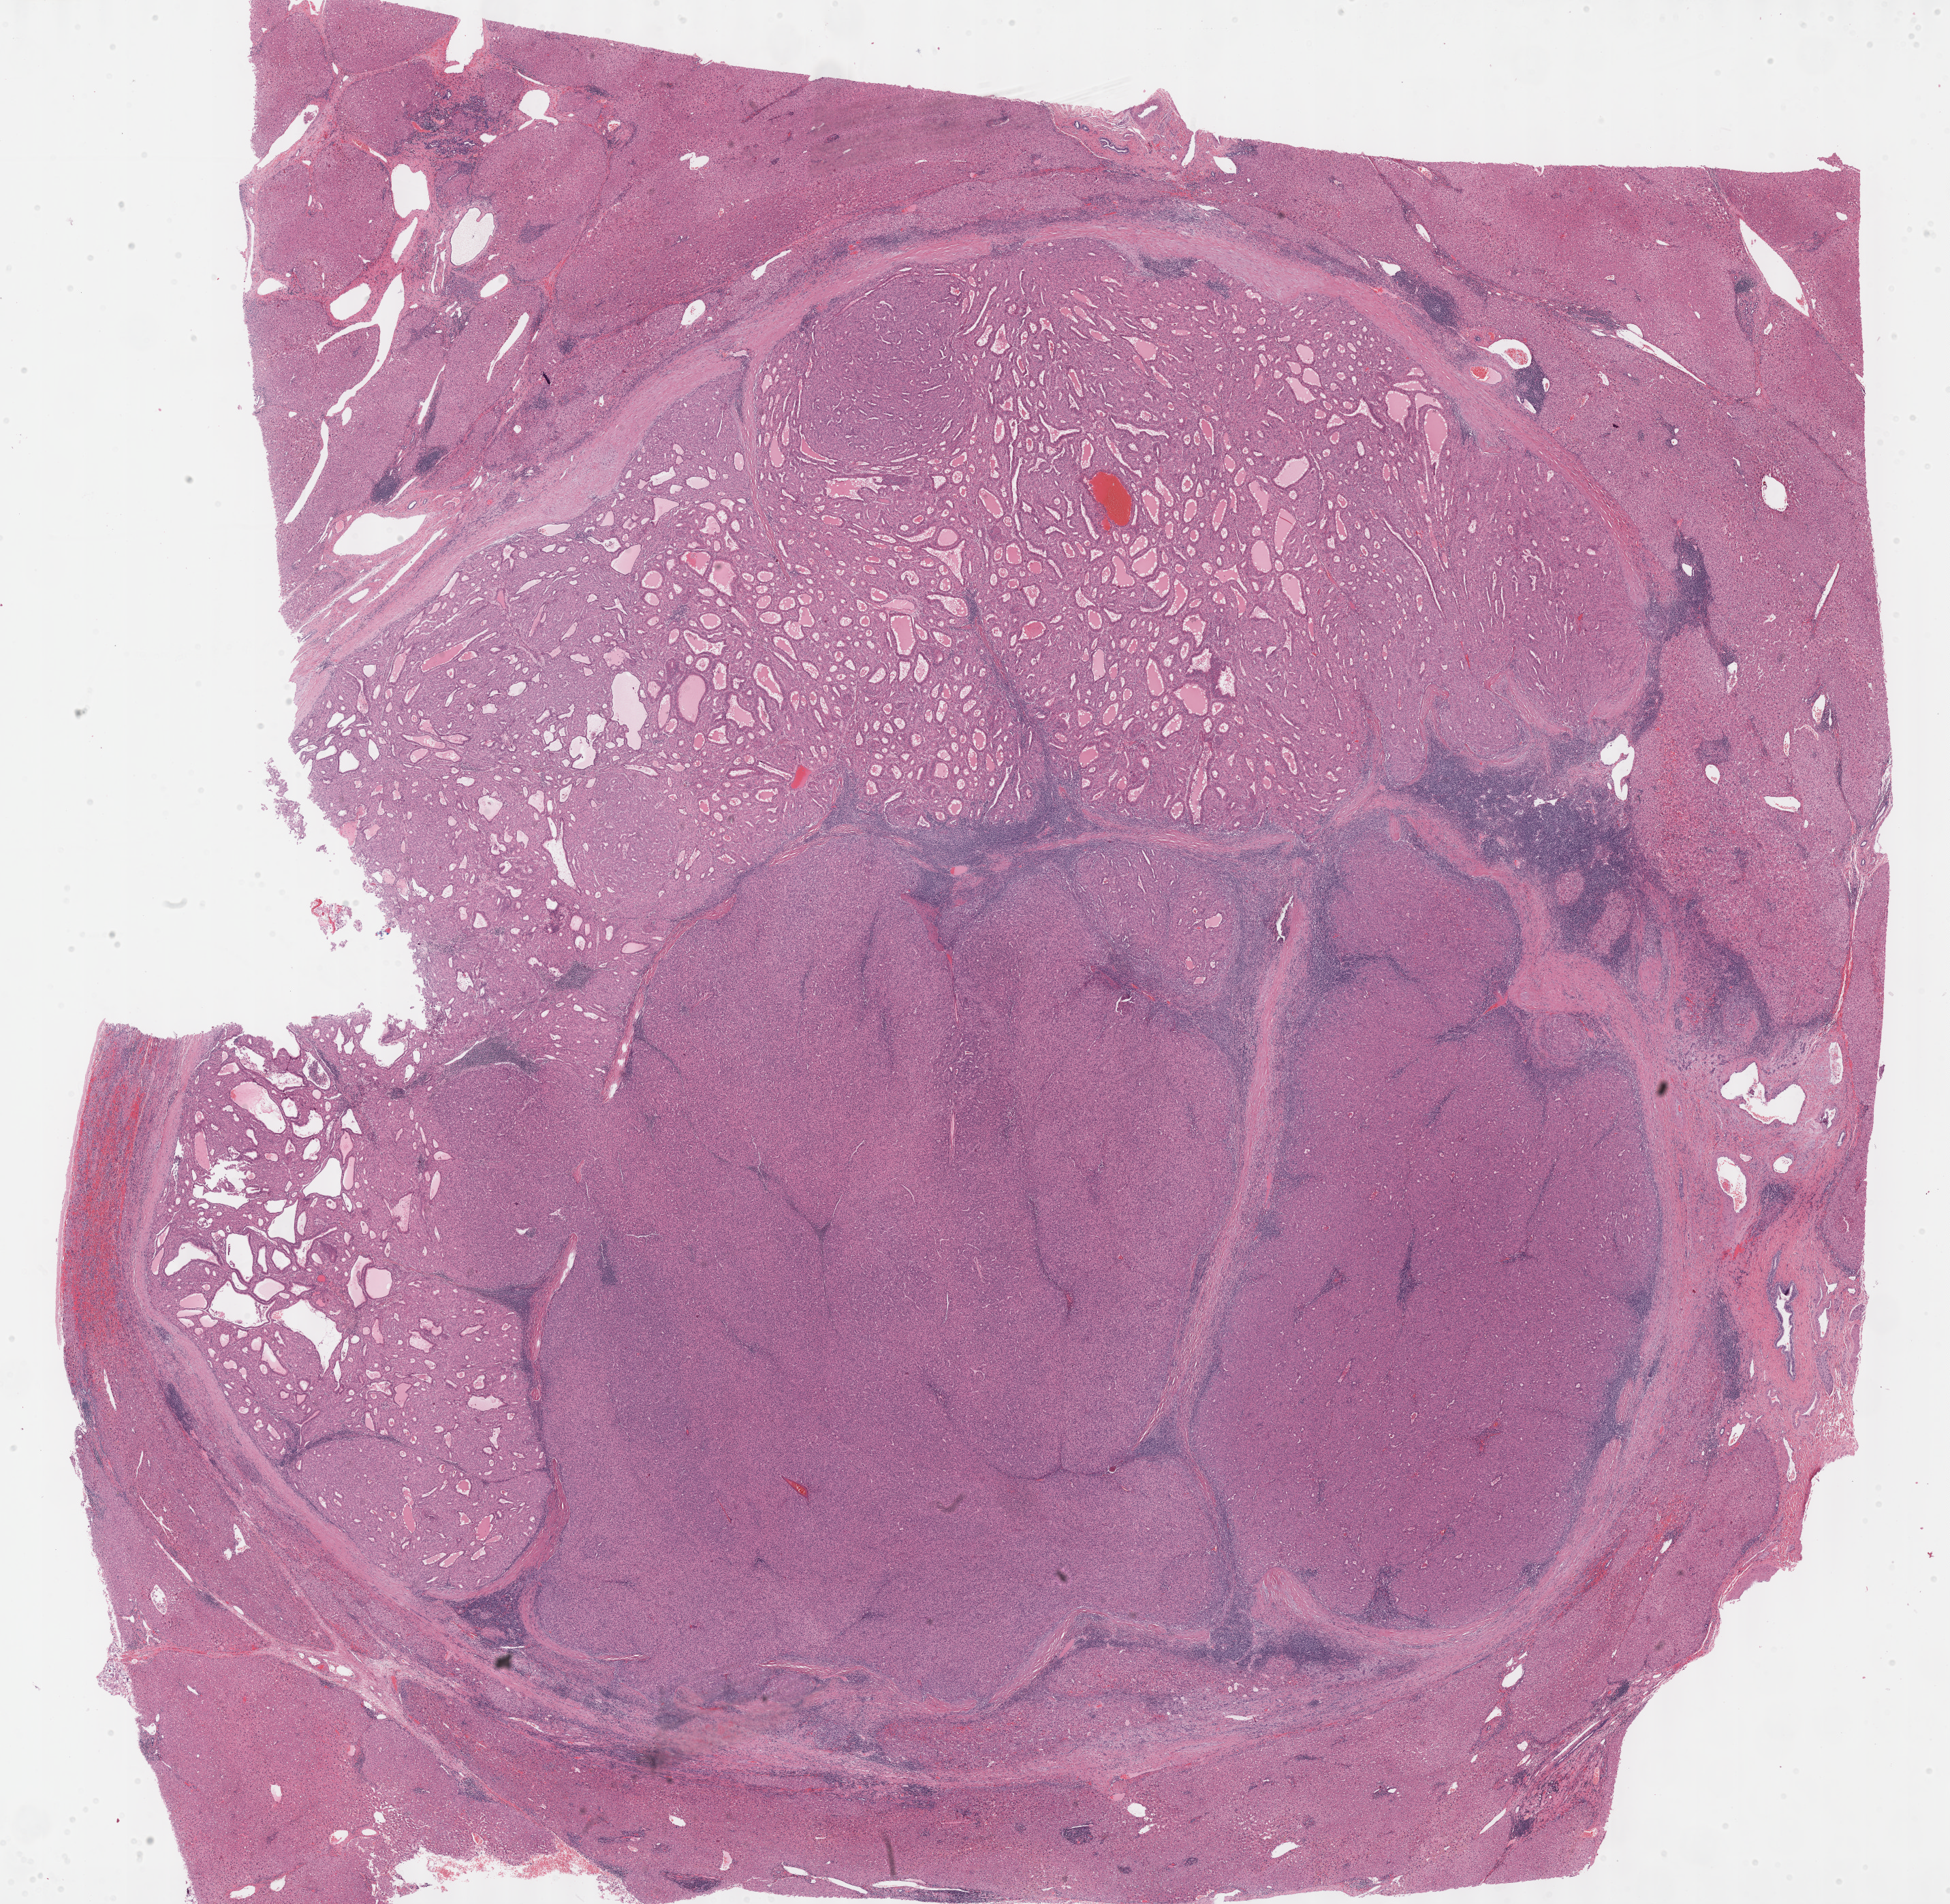
H&E whole-slide image — a low-resolution overview of the entire scanned area, about 23.1 x 22.6 mm, formalin-fixed paraffin-embedded (FFPE) diagnostic section, sample: primary tumour, liver. Male, age 61 years at initial diagnosis. Histologic grade: G2 (moderately differentiated).
AJCC pathologic stage: I (7th edition). Diagnosis: Hepatocellular carcinoma, NOS.